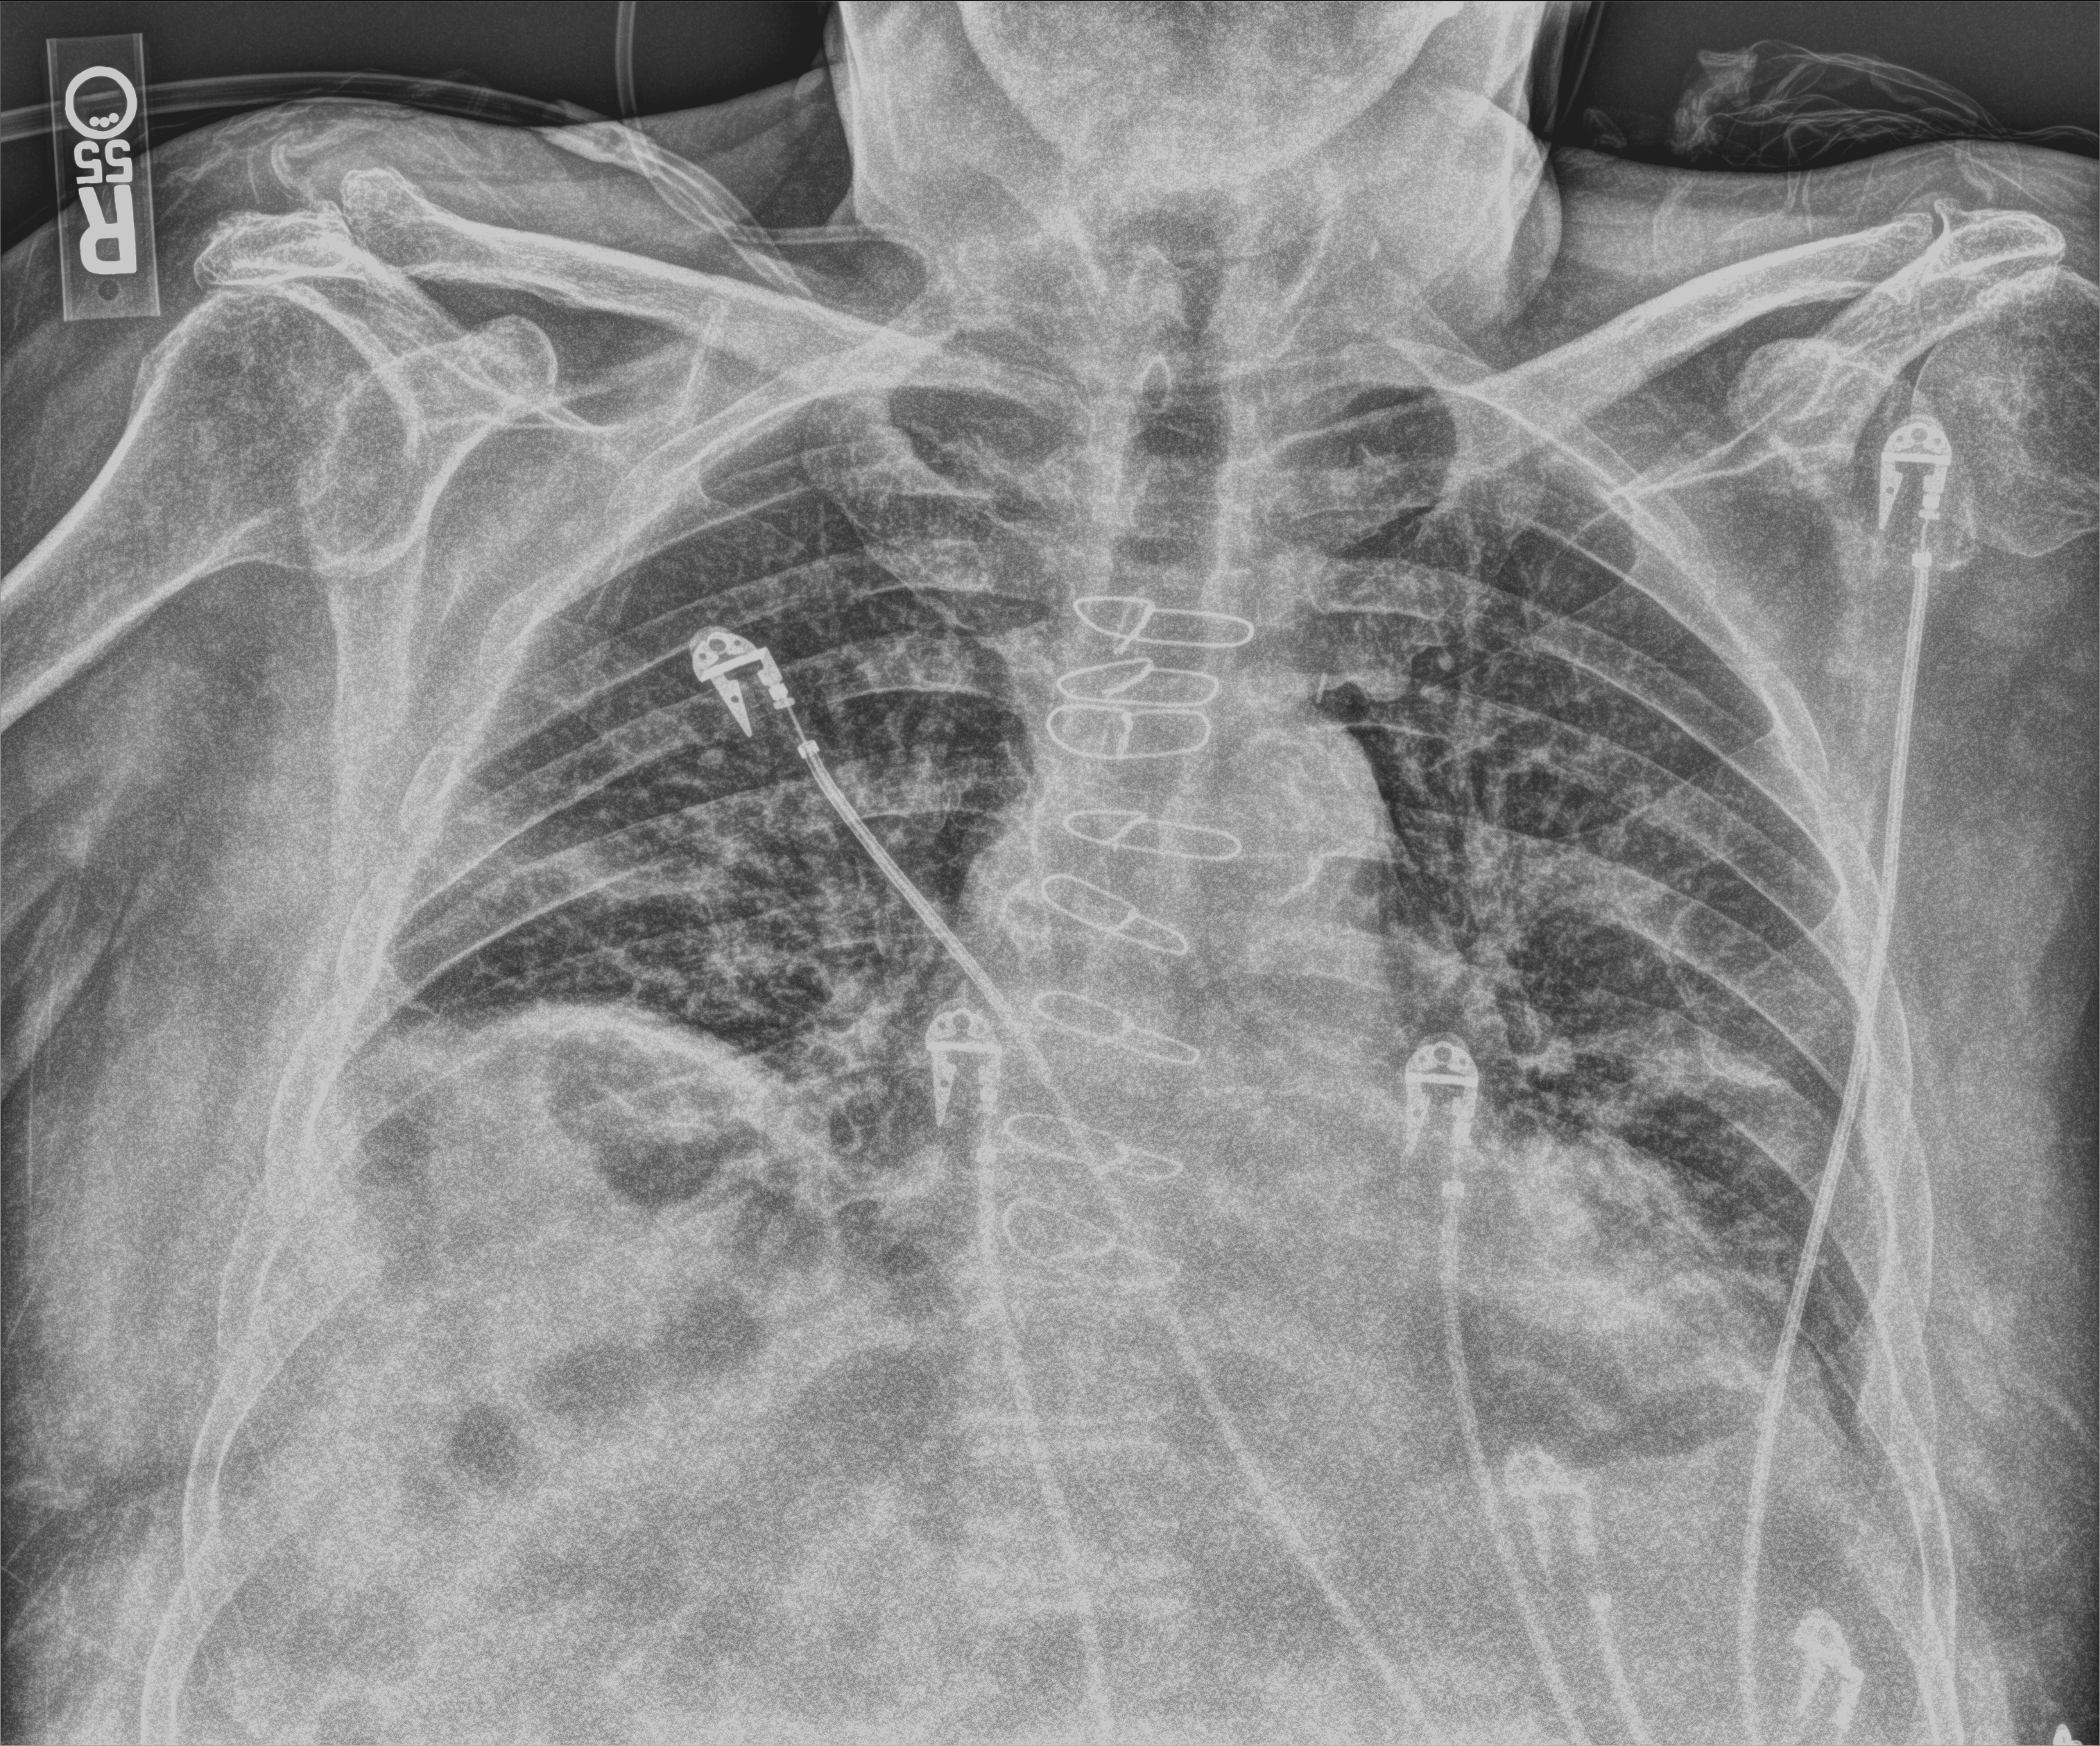
Bedside chest radiograph (computed radiography), anteroposterior (AP) projection. Male patient hospitalised with COVID-19, age 75–90 years.
Hospital-stay facts (about this admission, not read from this image; timing relative to this image not recorded):
- other chronic lung disease (admission record): no